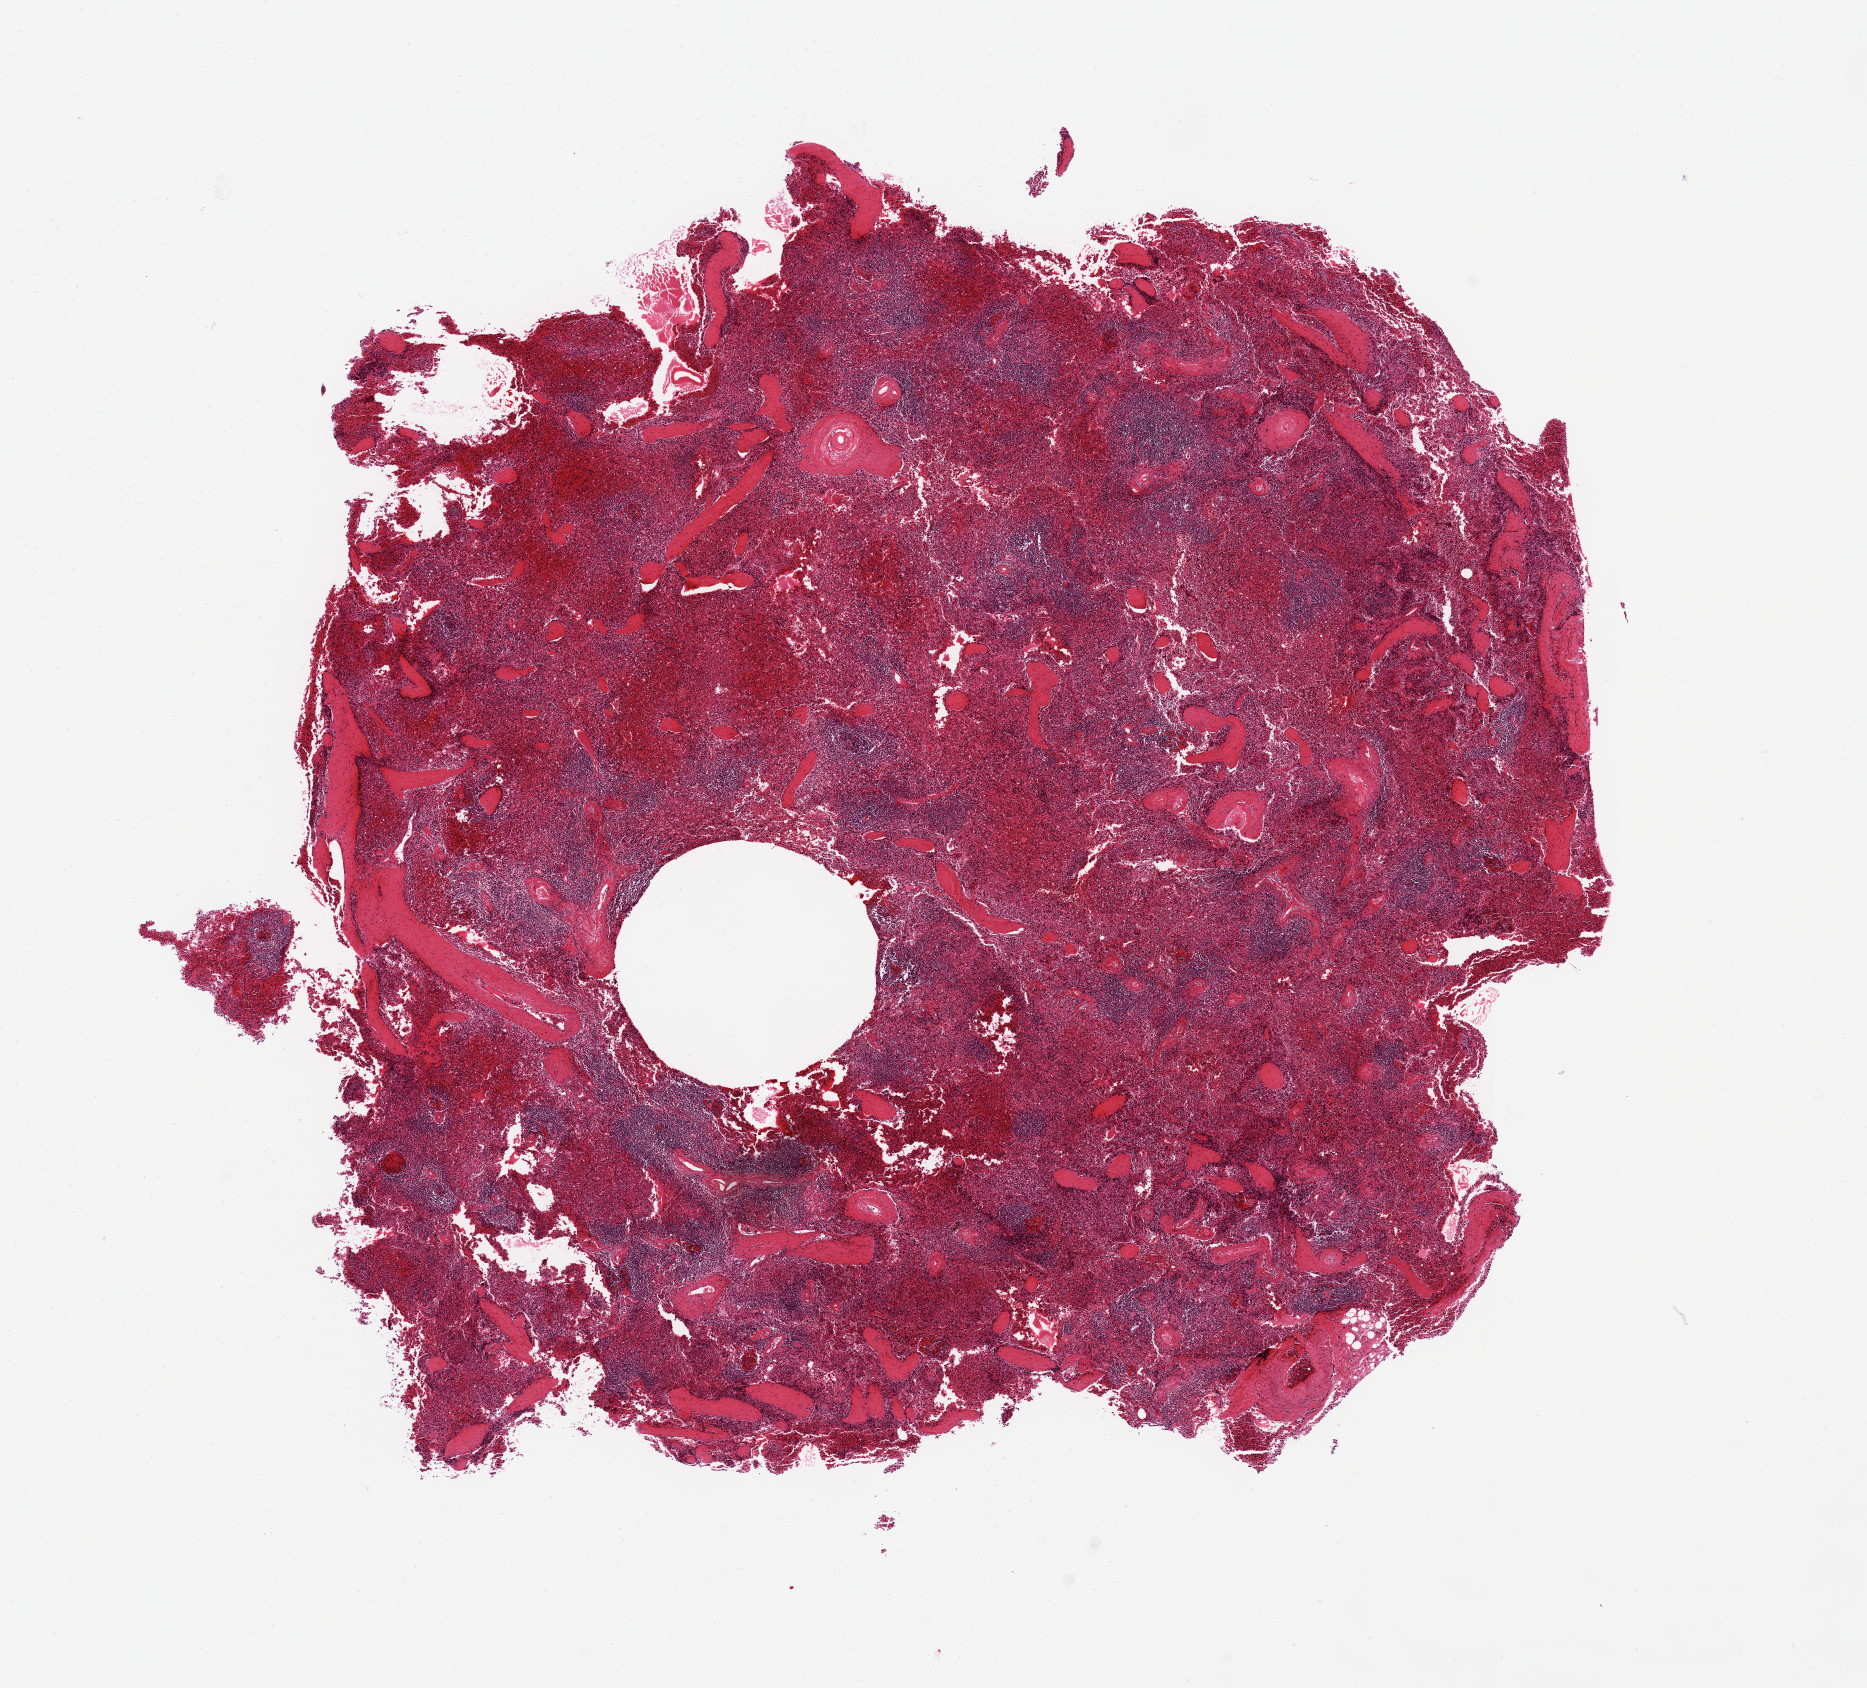
H&E whole-slide image, brightfield — low-resolution overview of the scanned area, about 14.8 x 13.4 mm, PAXgene-fixed paraffin-embedded (PFPE) section, section of spleen (target tissue), tissue donor sample. Donor sex: male.
* reviewer comment on this tissue sample: 9.9x9.6mm